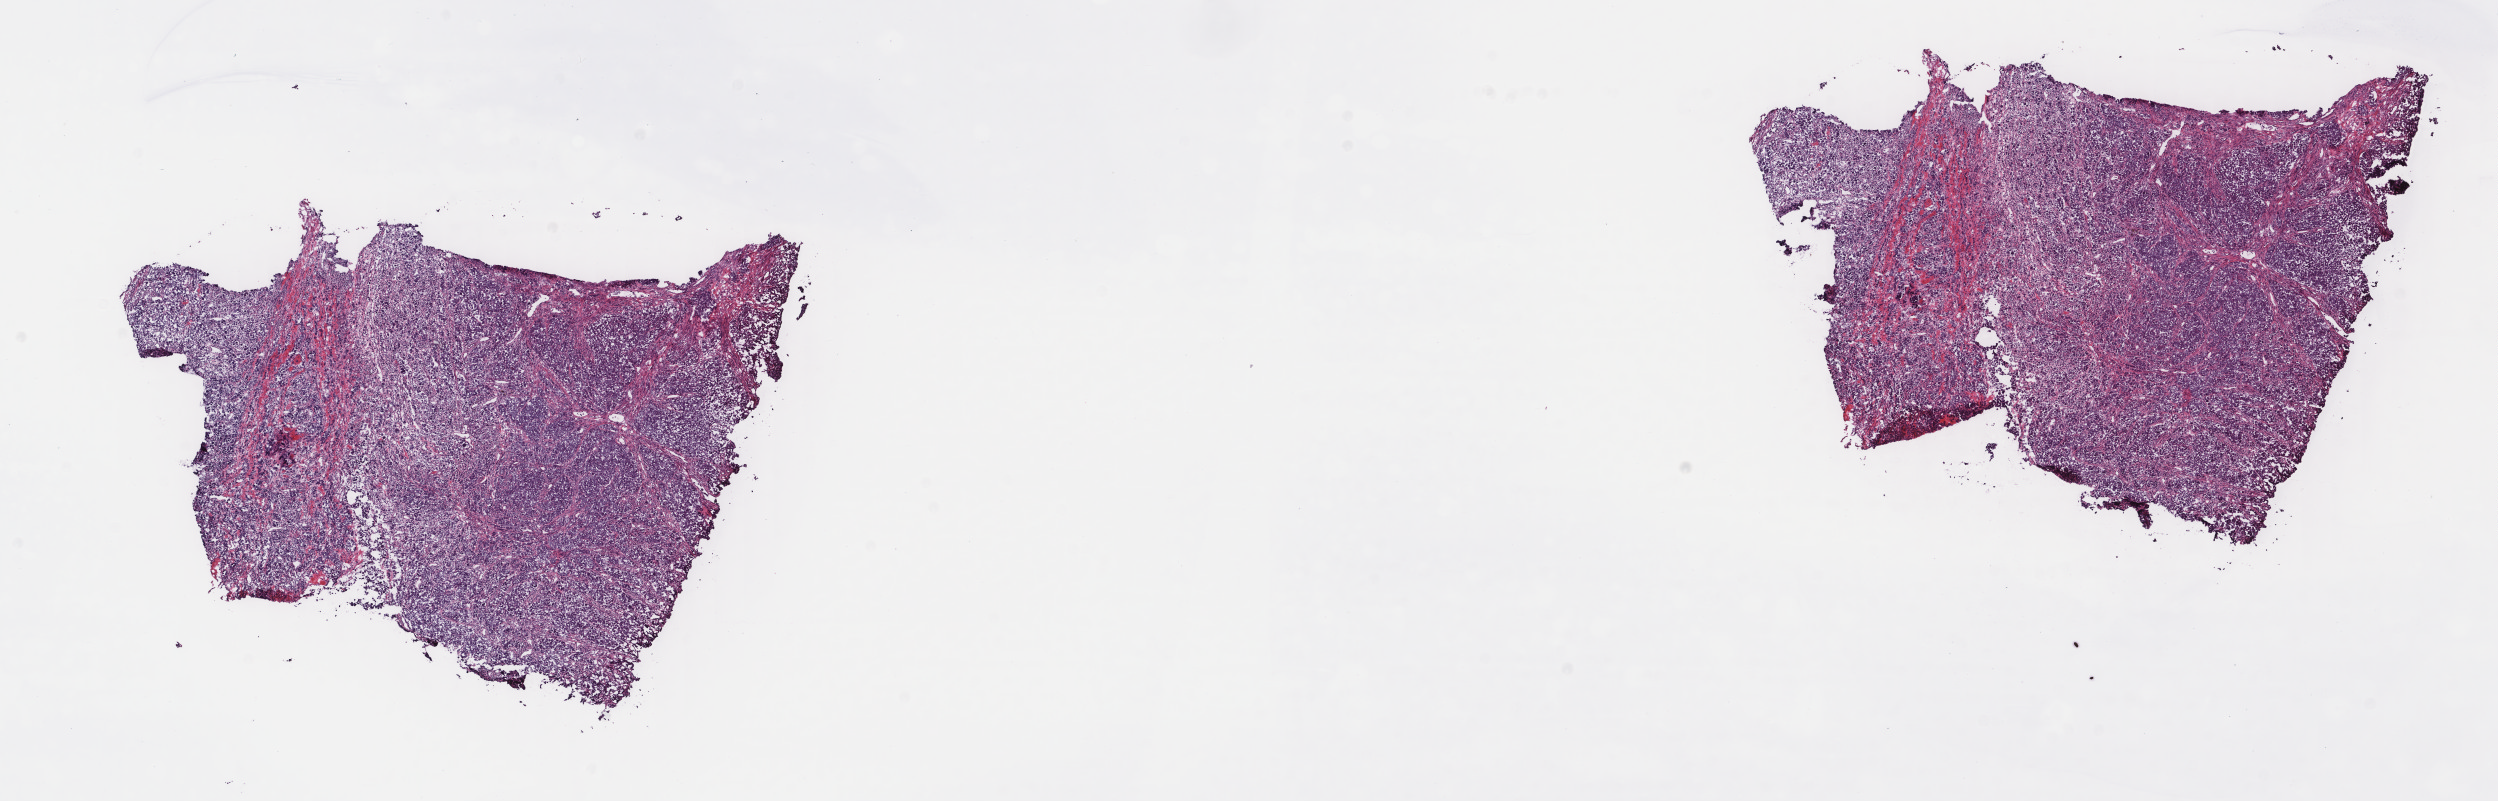
H&E-stained whole-slide image — low-resolution overview of the scanned area, about 19.8 x 6.4 mm, frozen section, metastatic tumour sample, sampled site not recorded. Patient: female, age at initial diagnosis 63 years. Slide review estimates, as recorded: tumour cells 85%, tumour nuclei 85%, normal cells 0%, stromal cells 15%, necrosis 0%. Infiltration values recorded for this section: lymphocyte infiltration 2%, monocyte infiltration 1%, neutrophil infiltration 0%.
This section: metastatic tumour tissue. Patient diagnosis: Malignant melanoma, NOS.